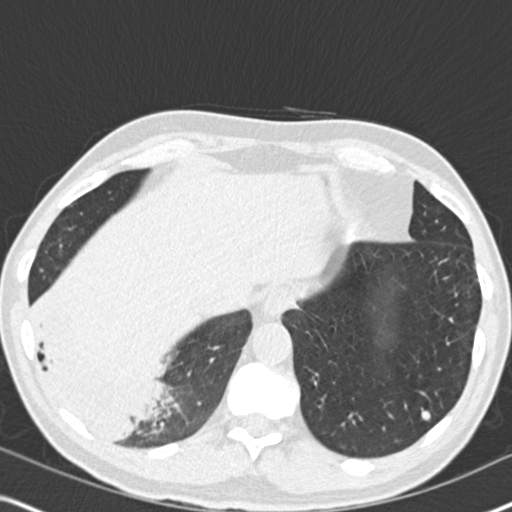
Low-dose screening chest CT, axial slice. Second annual screen. Lung window (W 1500 / L -600 HU). Slice 131 of 182 in the series. Male, age 61 years at enrolment.
Expert reader's lesion annotation, bounding box [x1, y1, x2, y2] px = [19, 280, 180, 455]. Reader record for this screening exam (exam-level; its link to the box is not recorded): non-calcified nodule or mass ≥4 mm, right lower lobe, 90 × 80 mm, soft tissue attenuation, pre-existing on the prior screen: yes; interval growth: yes. Lung cancer was diagnosed 20 days after this screen: bronchiolo-alveolar adenocarcinoma, NOS, right lower lobe, moderately differentiated (G2), stage IIIB (AJCC 6th edition), 90 mm at pathology.